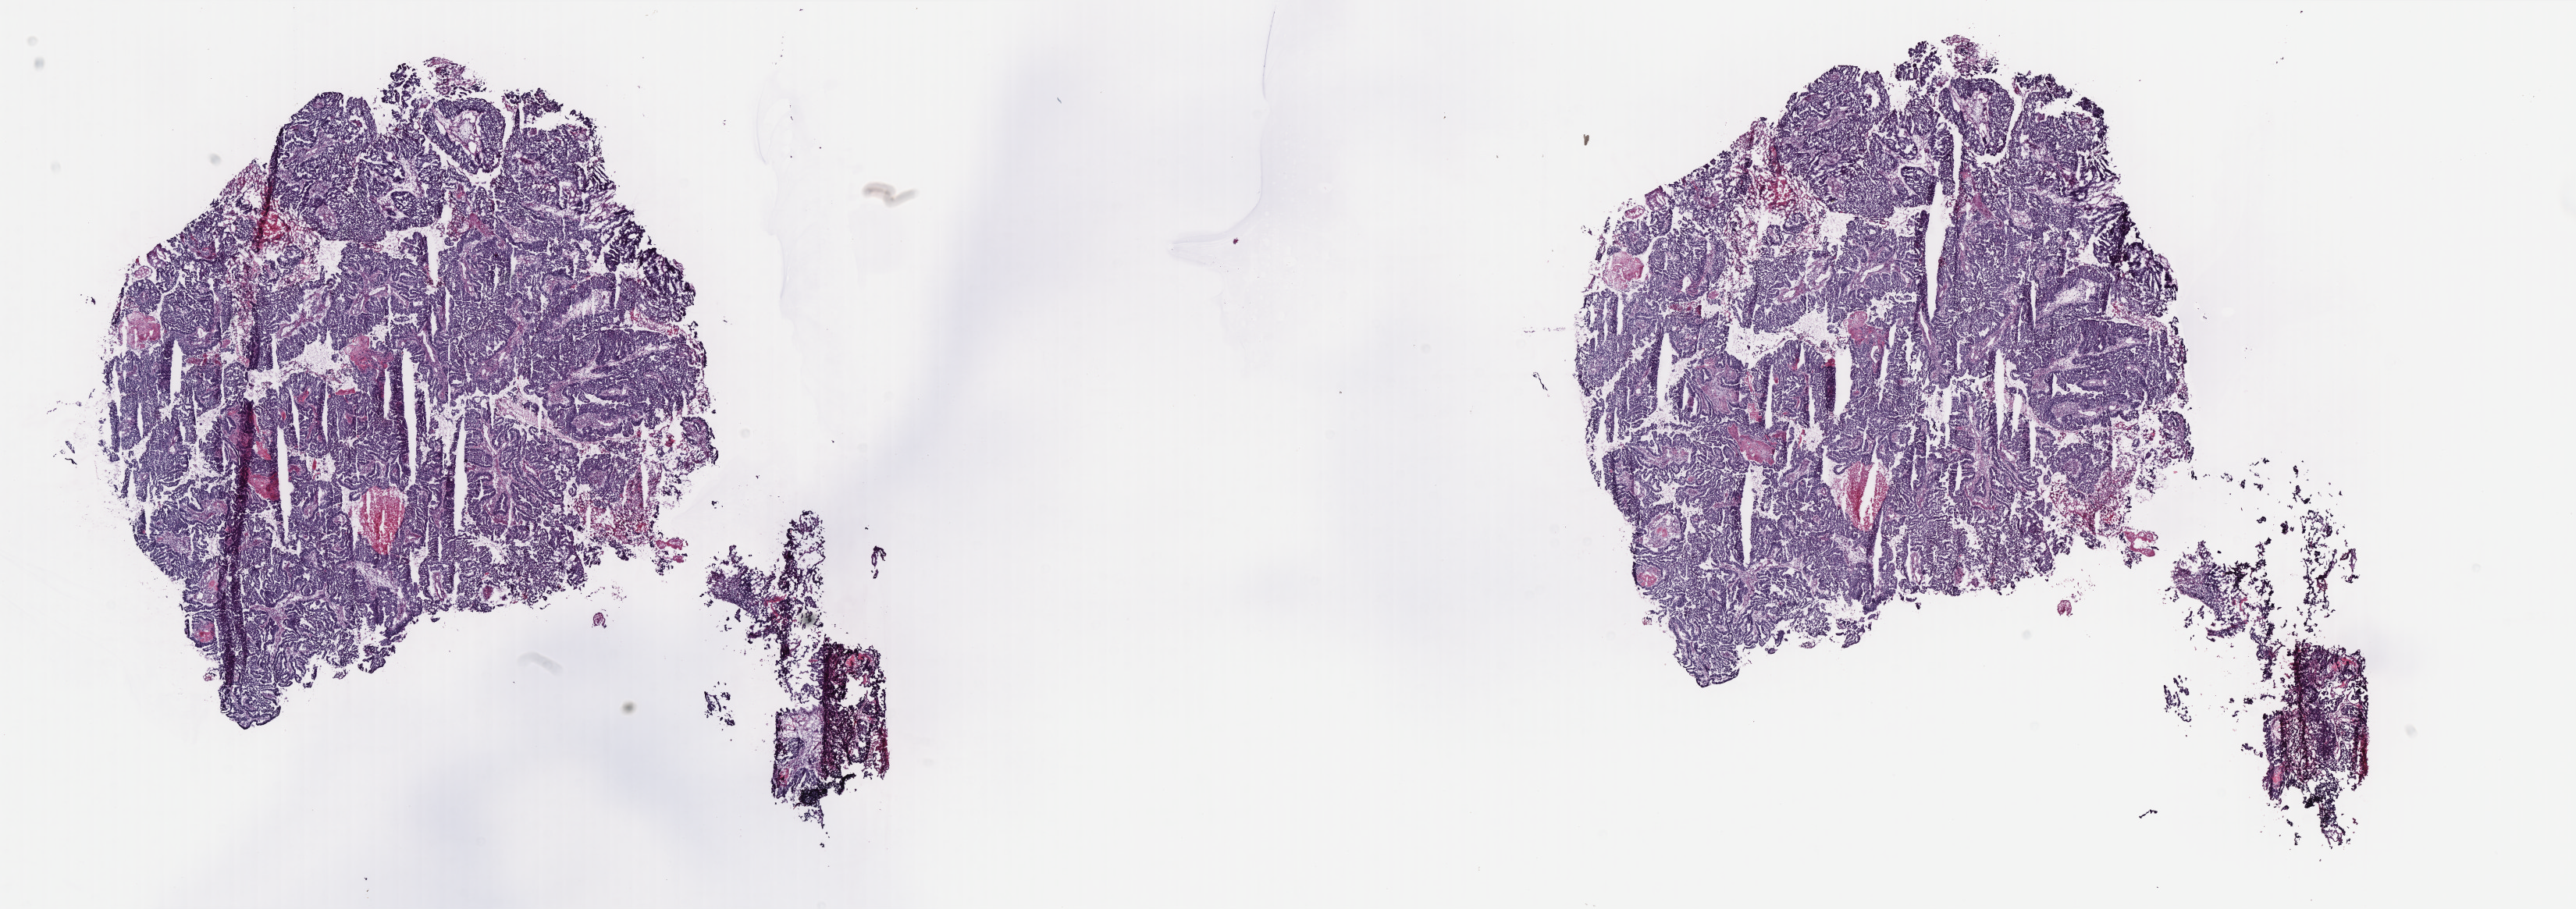
Whole-slide histology image, H&E — a low-resolution overview of the entire scanned area, about 26.5 x 9.3 mm (from a 40x scan); frozen section from the bottom of the tissue portion; primary tumour sample from the uterus. Patient: female, age at initial diagnosis 57 years. Histologic grade: G3 (poorly differentiated). Slide review estimates, as recorded: tumour cells 75%, tumour nuclei 95%, normal cells 5%, stromal cells 0%, necrosis 20%. Inflammatory infiltration, as recorded: lymphocyte infiltration 20%, monocyte infiltration 0%, neutrophil infiltration 10%.
FIGO stage: IA. Pathologic diagnosis: Endometrioid adenocarcinoma, NOS.